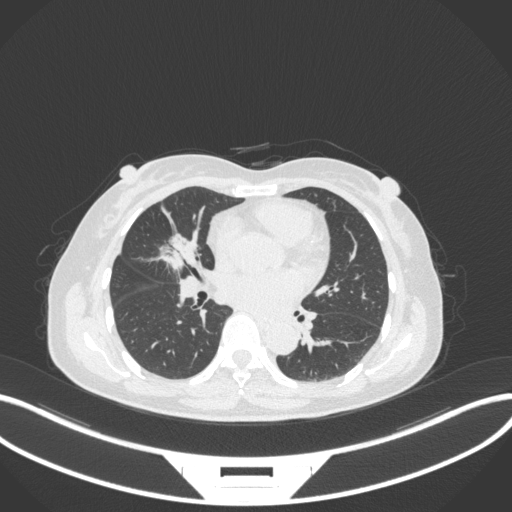
Chest CT, one axial slice; reconstruction kernel B31f; lung window (W 1500 / L -600 HU); 1 mm slice thickness; 512 × 512 image matrix, field of view 400 × 400 mm. Patient: female, 51 years. Case-level facts recorded for this patient, not image findings: clinical TNM (as recorded): T1c N0 M0; histopathological grade: G2.
Outlined on this slice (rectangle marked by the reading radiologist):
- lung tumour (recorded histology: adenocarcinoma): bounding box <156,224,204,271> (left, top, right, bottom; pixels)